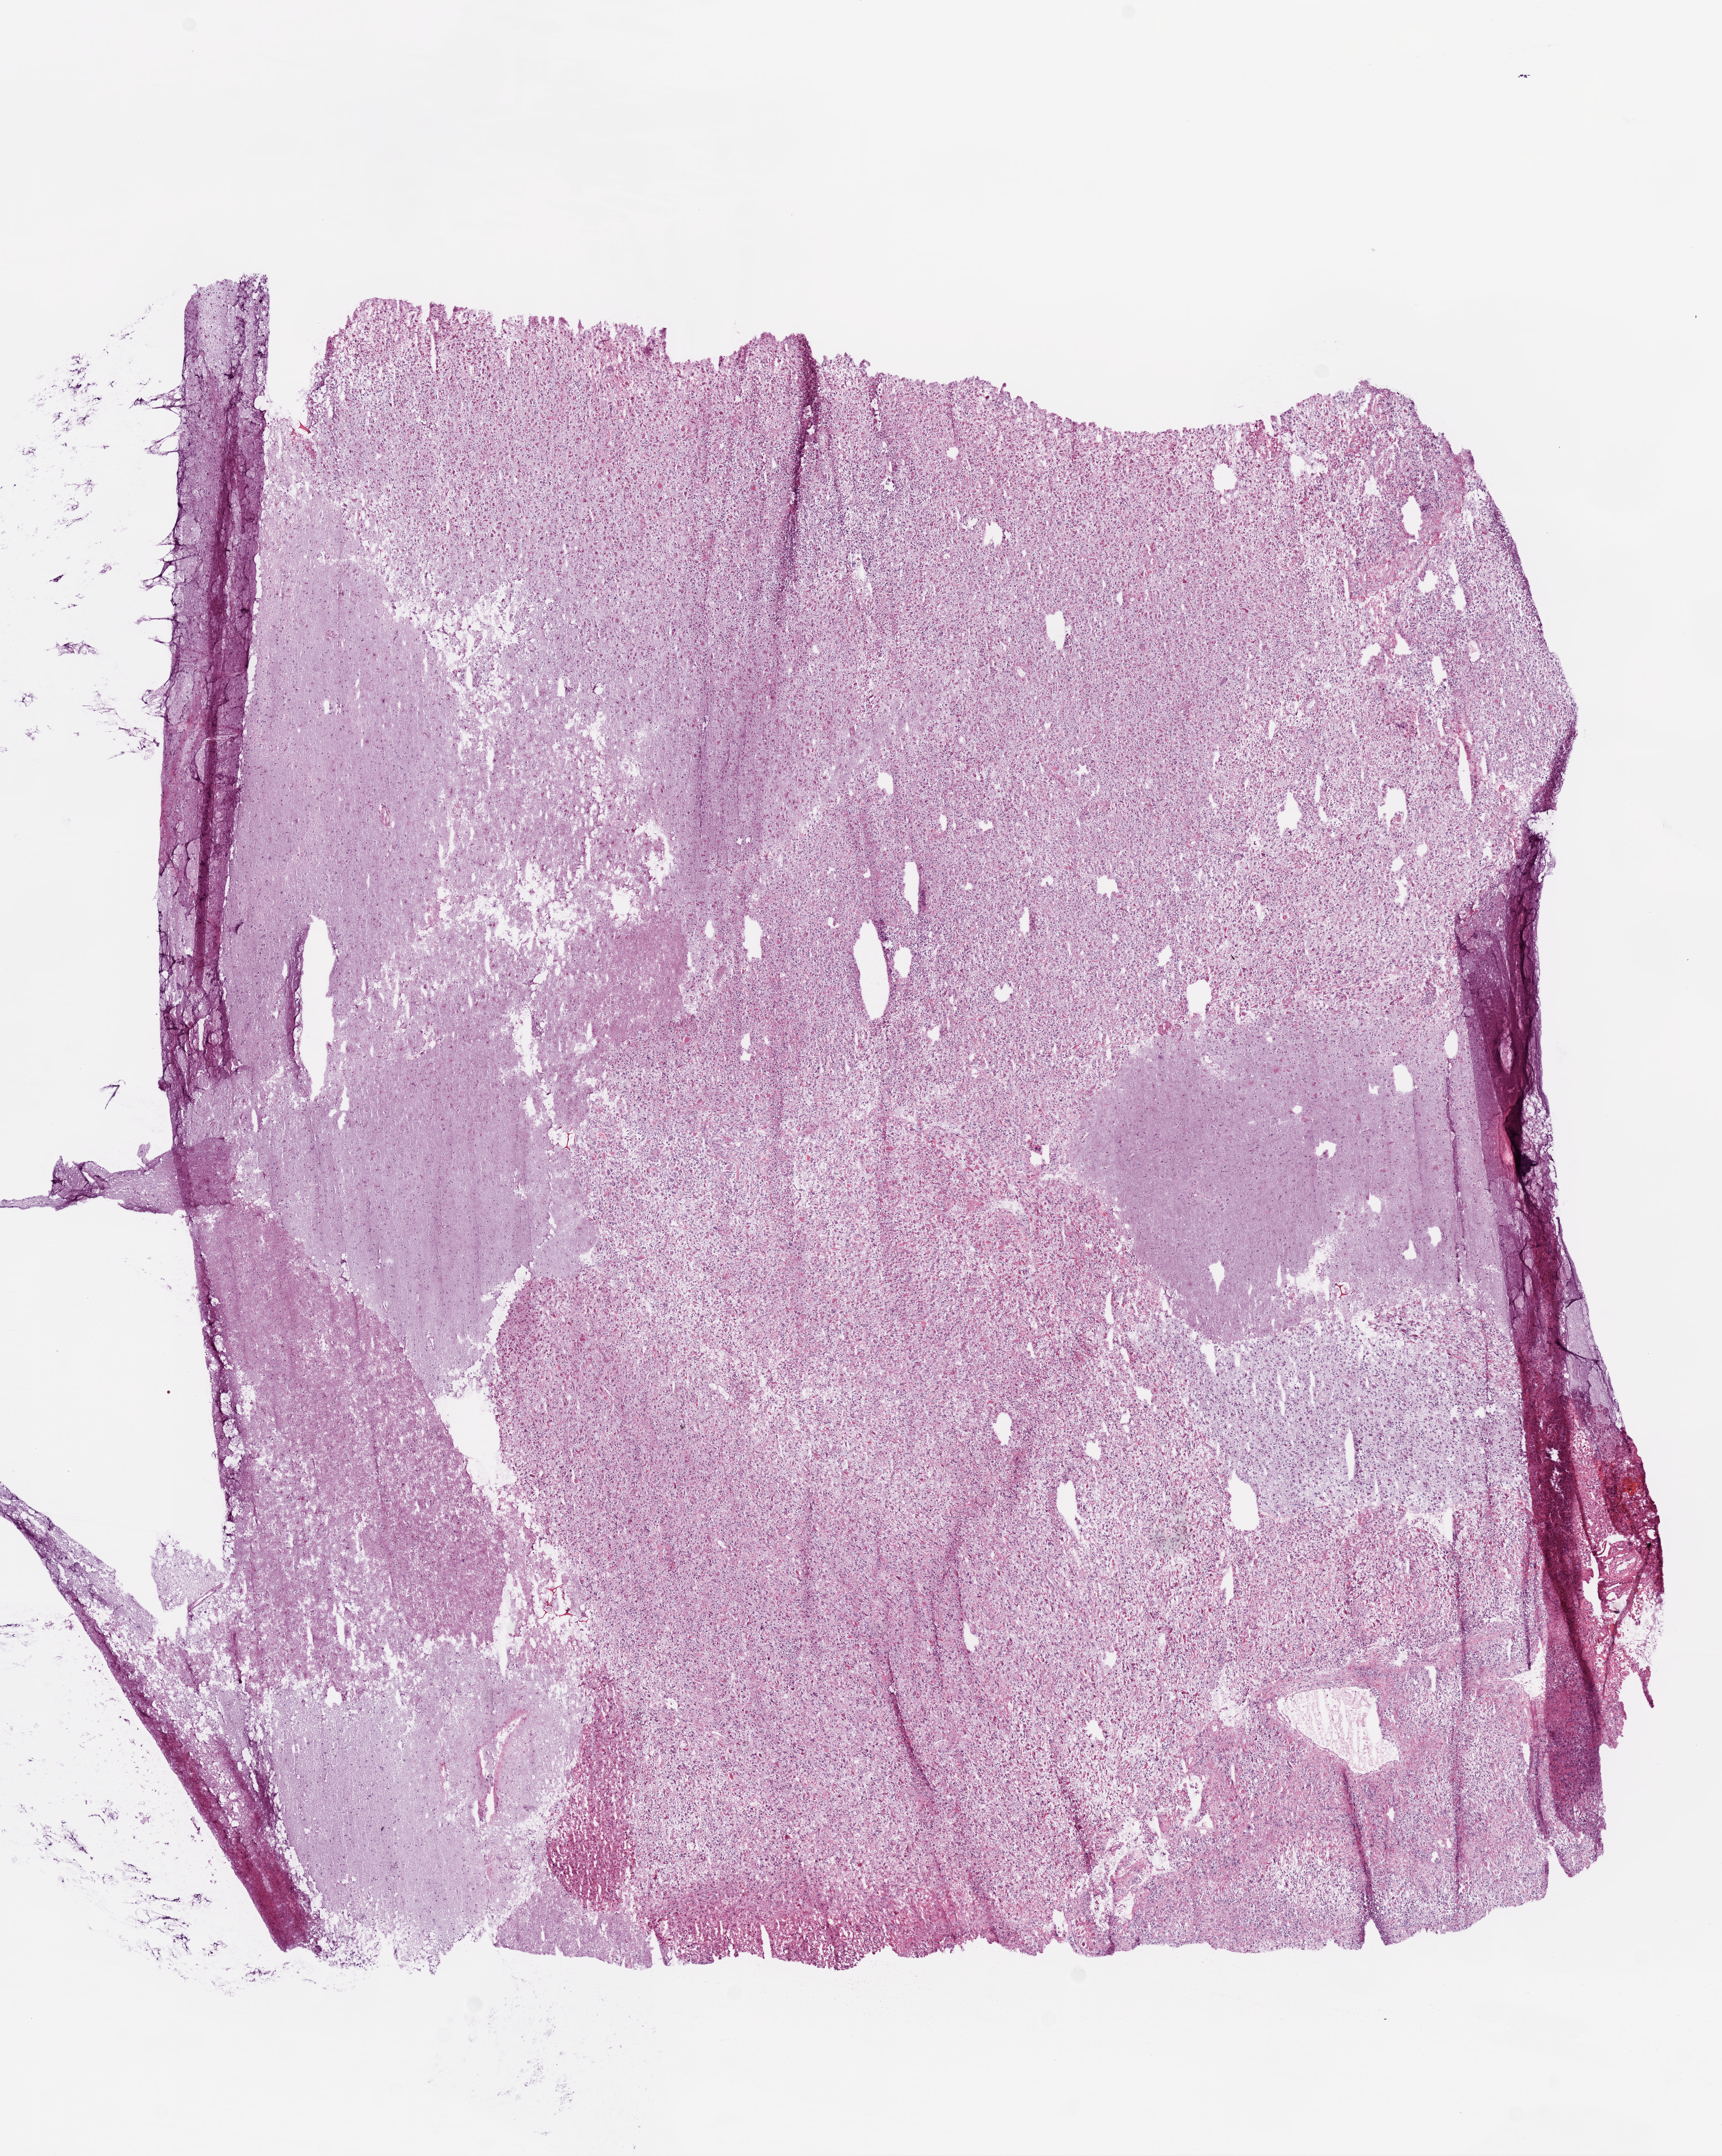
Digitized H&E tissue section (whole slide) — a low-resolution overview of the entire scanned area, about 10.0 x 12.6 mm (acquisition: 20x scan). Frozen section from the bottom of the tissue portion. Primary tumour sample from the brain. Female patient; age at initial diagnosis 53 years. Composition of this section per pathologist review: tumour cells 98%, tumour nuclei 80%, normal cells 0%, stromal cells 0%, necrosis 2%.
Diagnosis: Glioblastoma.